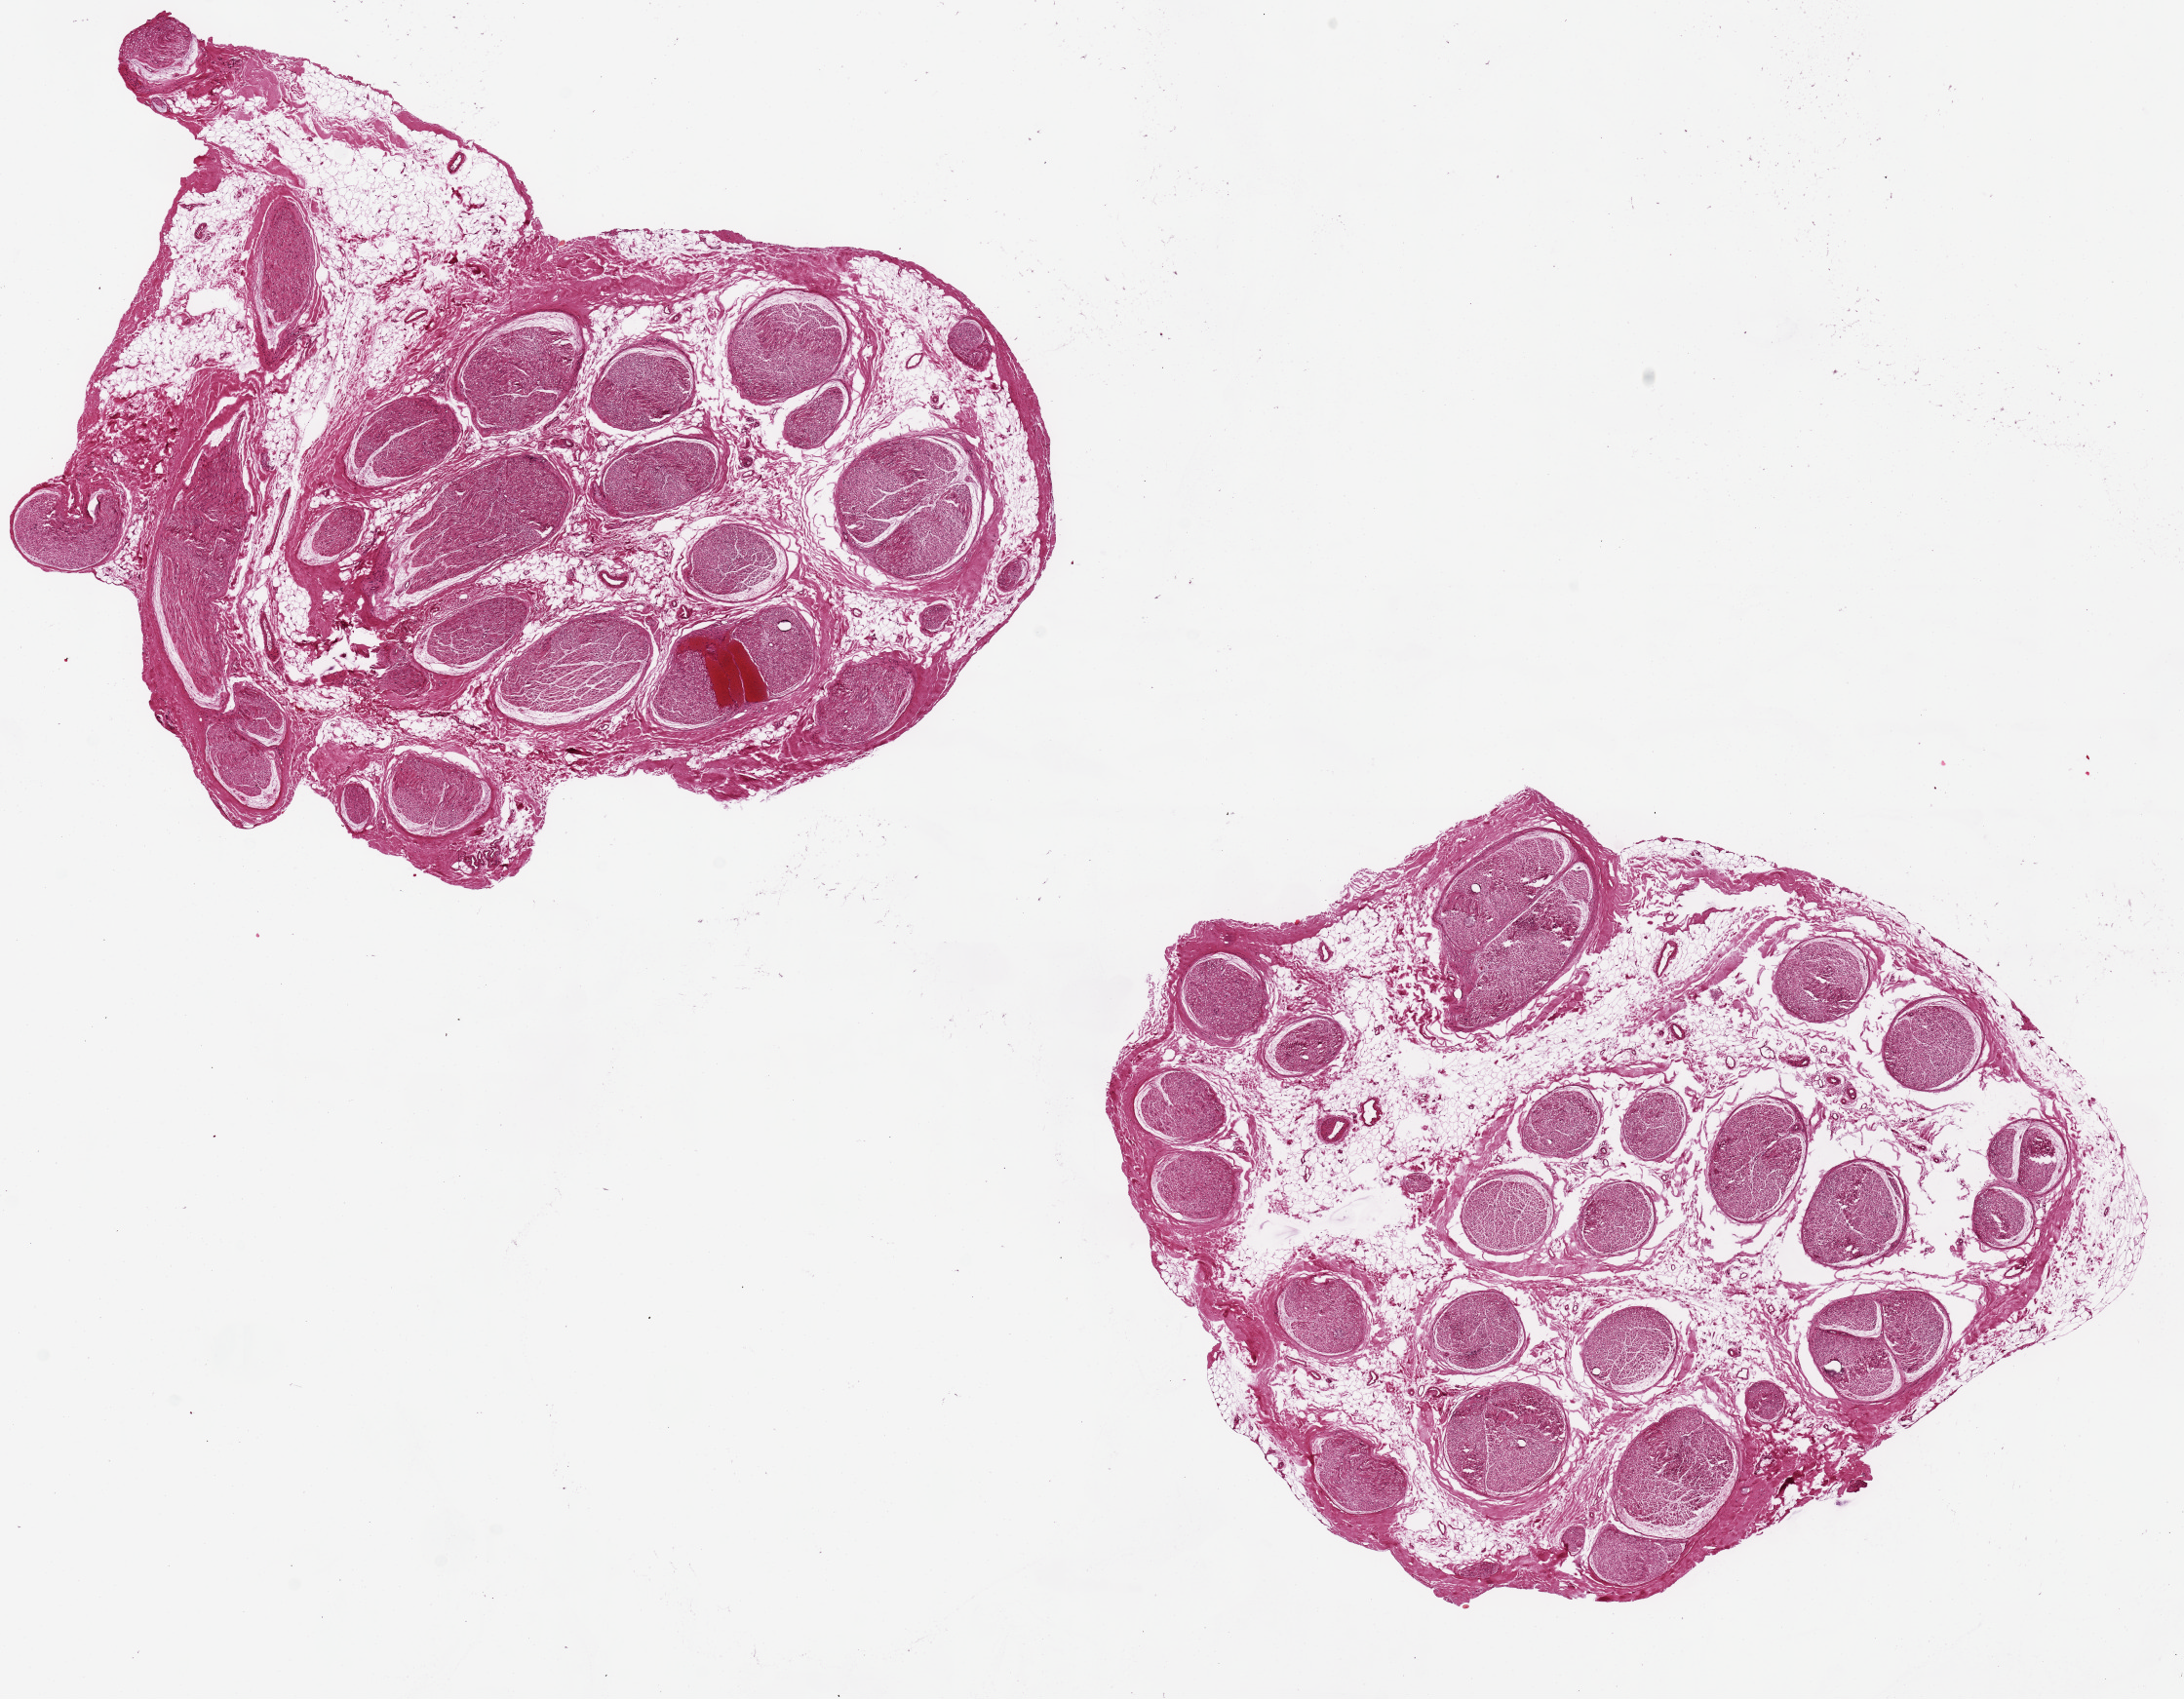
Whole-slide image, H&E stain, shown as a low-resolution overview of the whole scanned area (about 17.7 x 13.8 mm, acquisition: 20x scan). PAXgene-fixed, paraffin-embedded tissue. Target tissue: tibial nerve. Donor tissue sample.
Reviewer comment on this tissue sample: Nerve comprises 60% of tissue area; remainder is fibrofatty tissue.